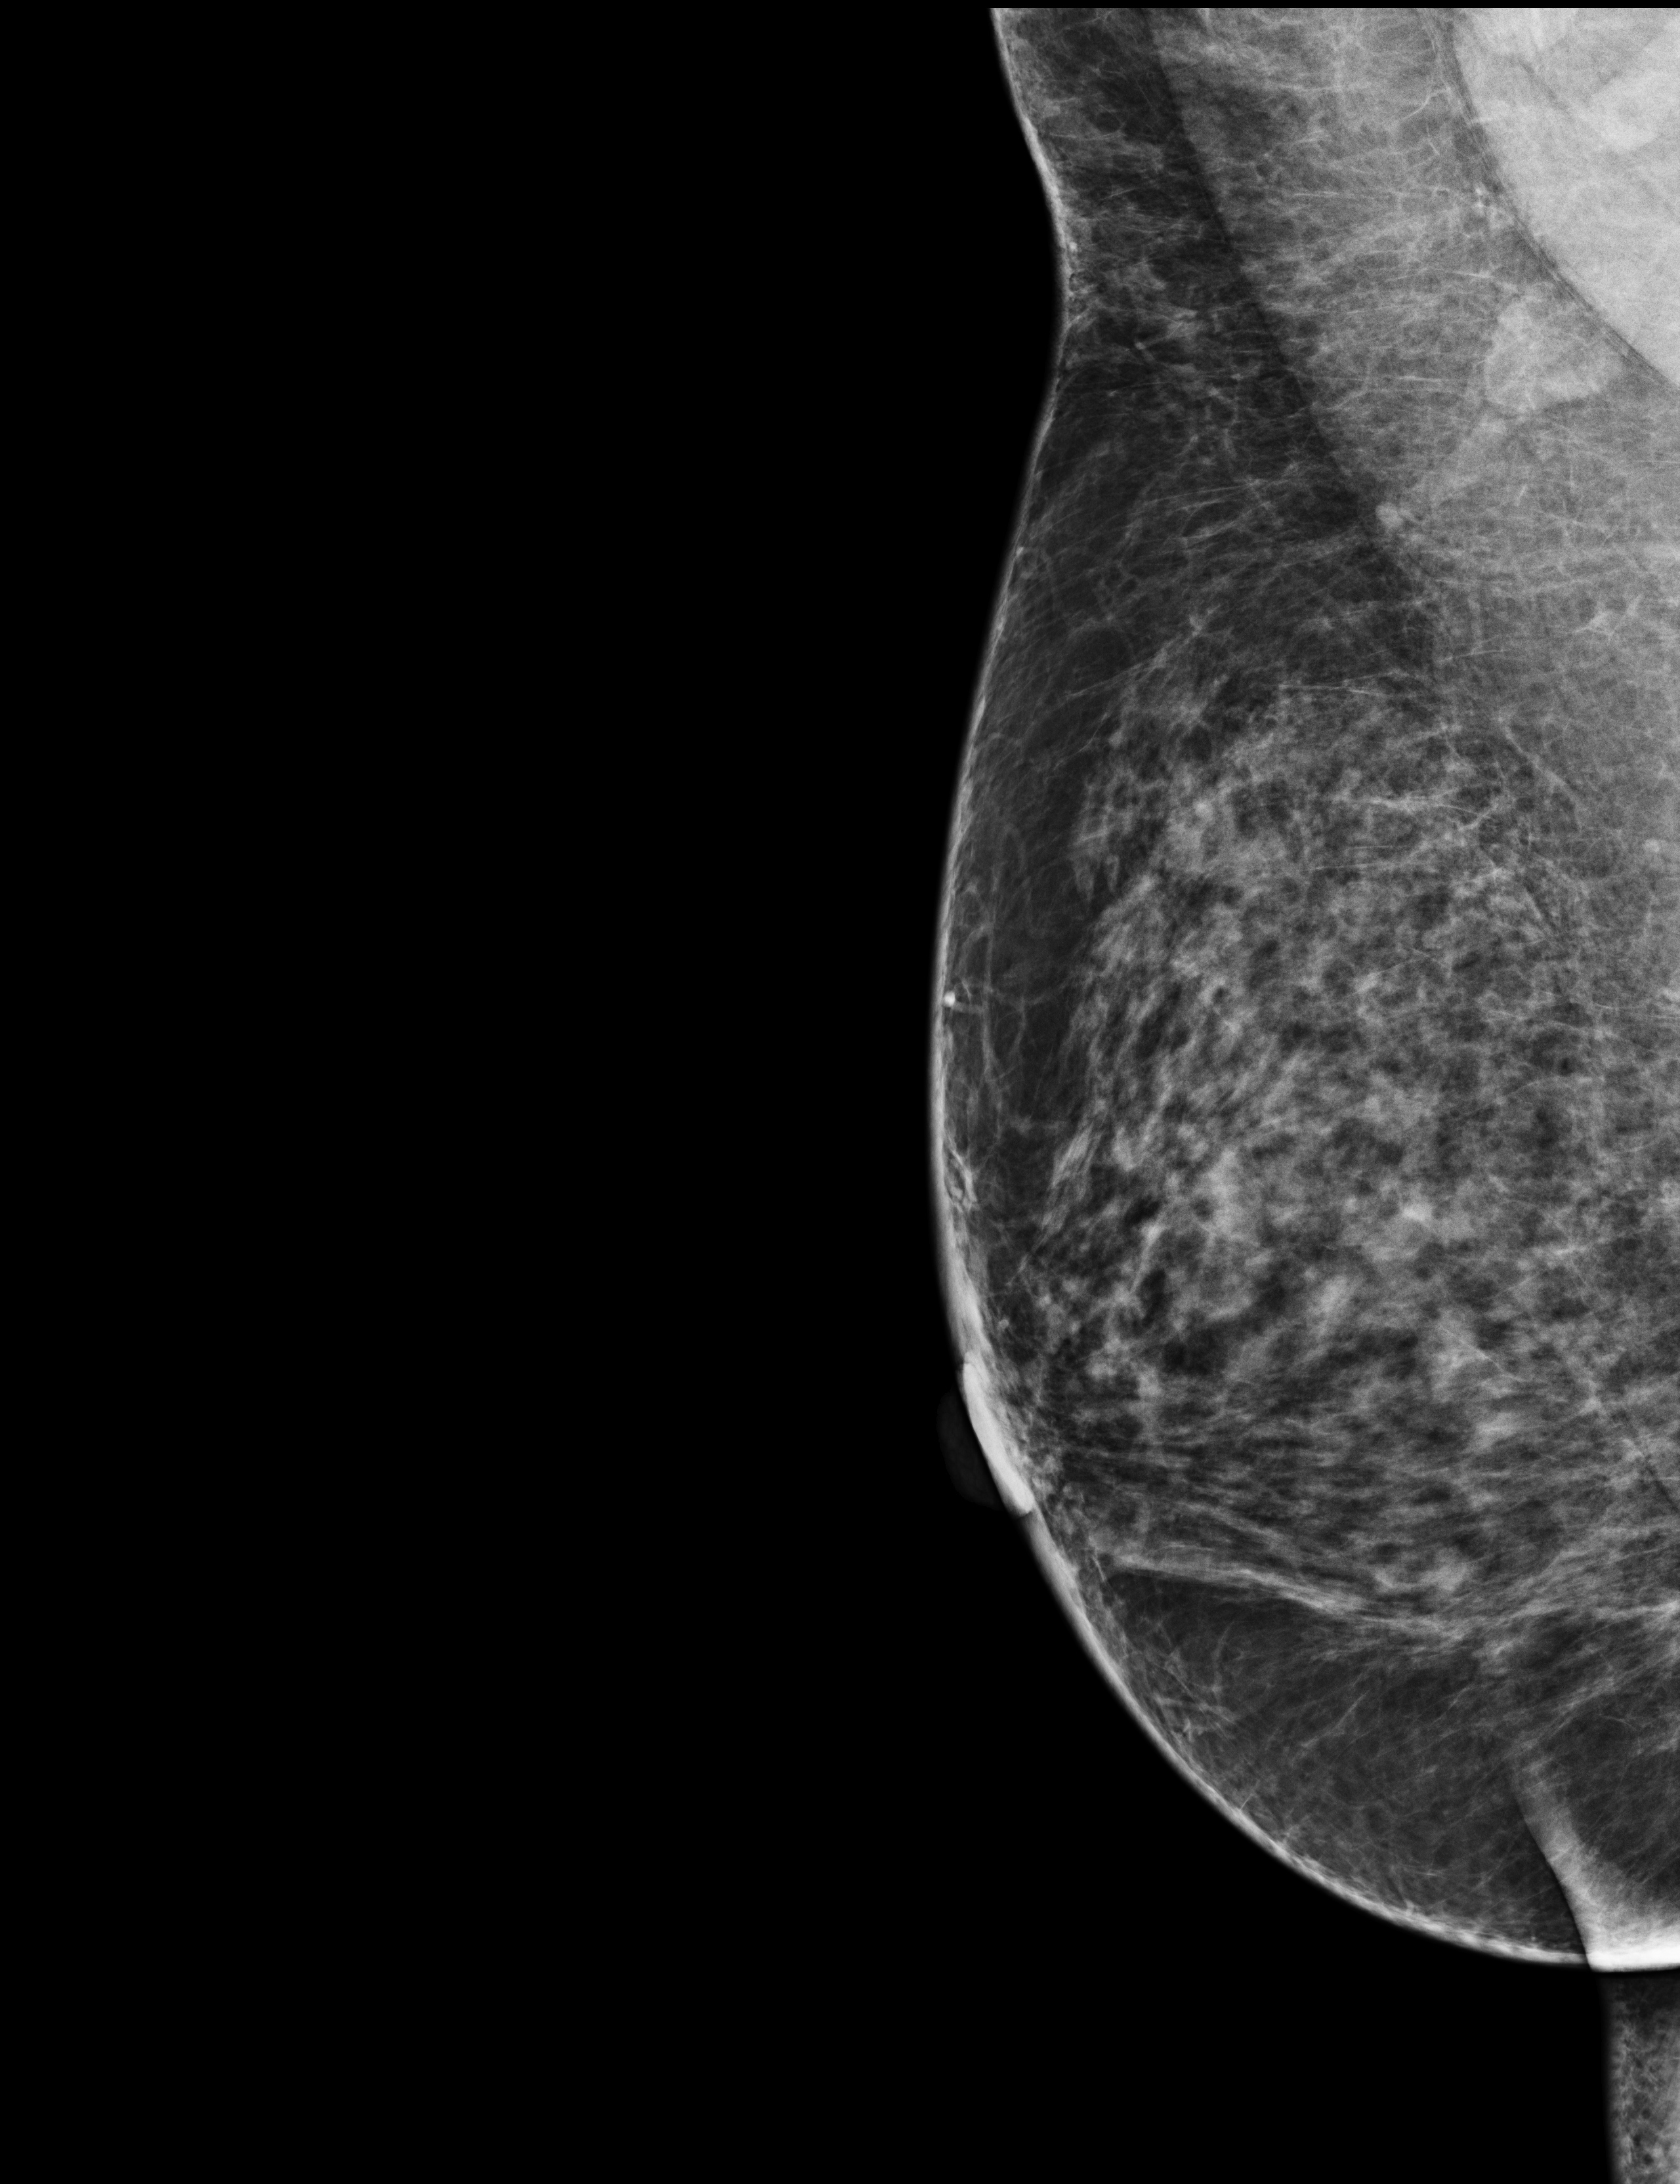
Annual screening mammography examination, system: Selenia Dimensions. Patient: female, 53 years.
Image type: full-field digital mammogram. Breast: right. Projection: medio-lateral oblique projection.